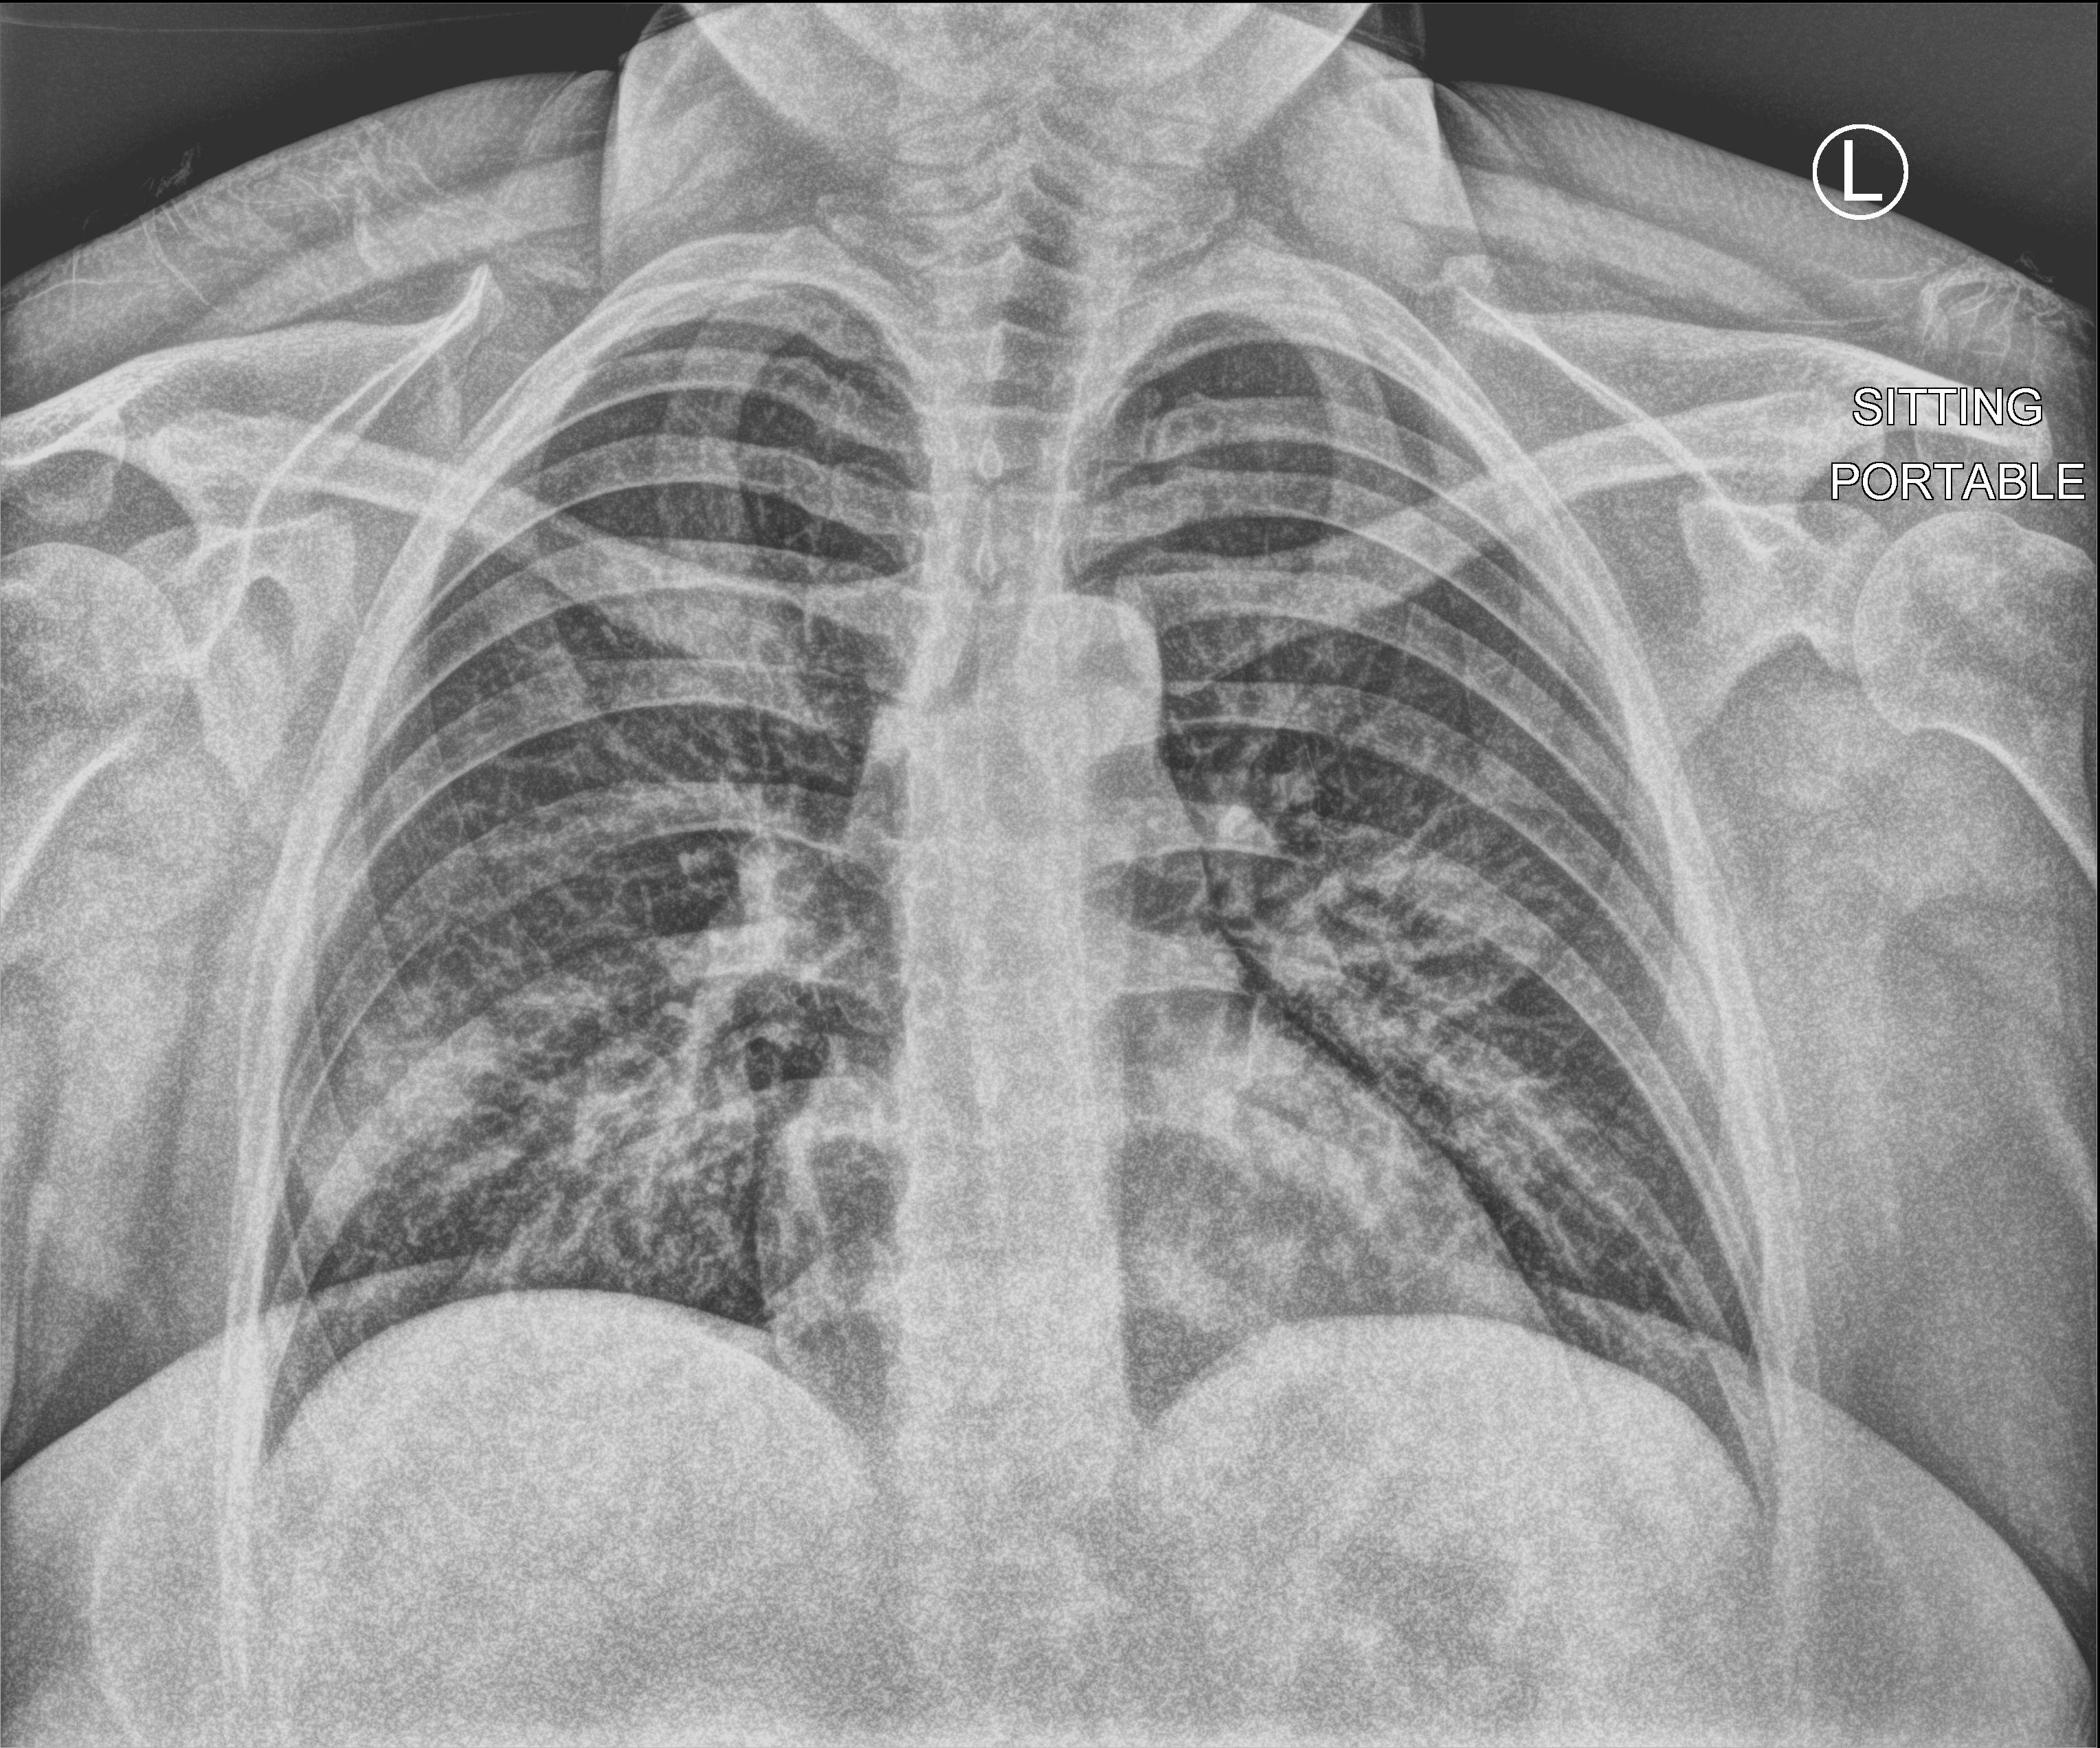
Chest X-ray (portable), anteroposterior (AP) projection. Patient hospitalised with COVID-19; female, aged 18–59 years.
From the hospital-stay record, not from the radiograph (when in the stay this image was taken is not recorded): diabetes (admission record): no; mechanically ventilated during this hospital stay: no.